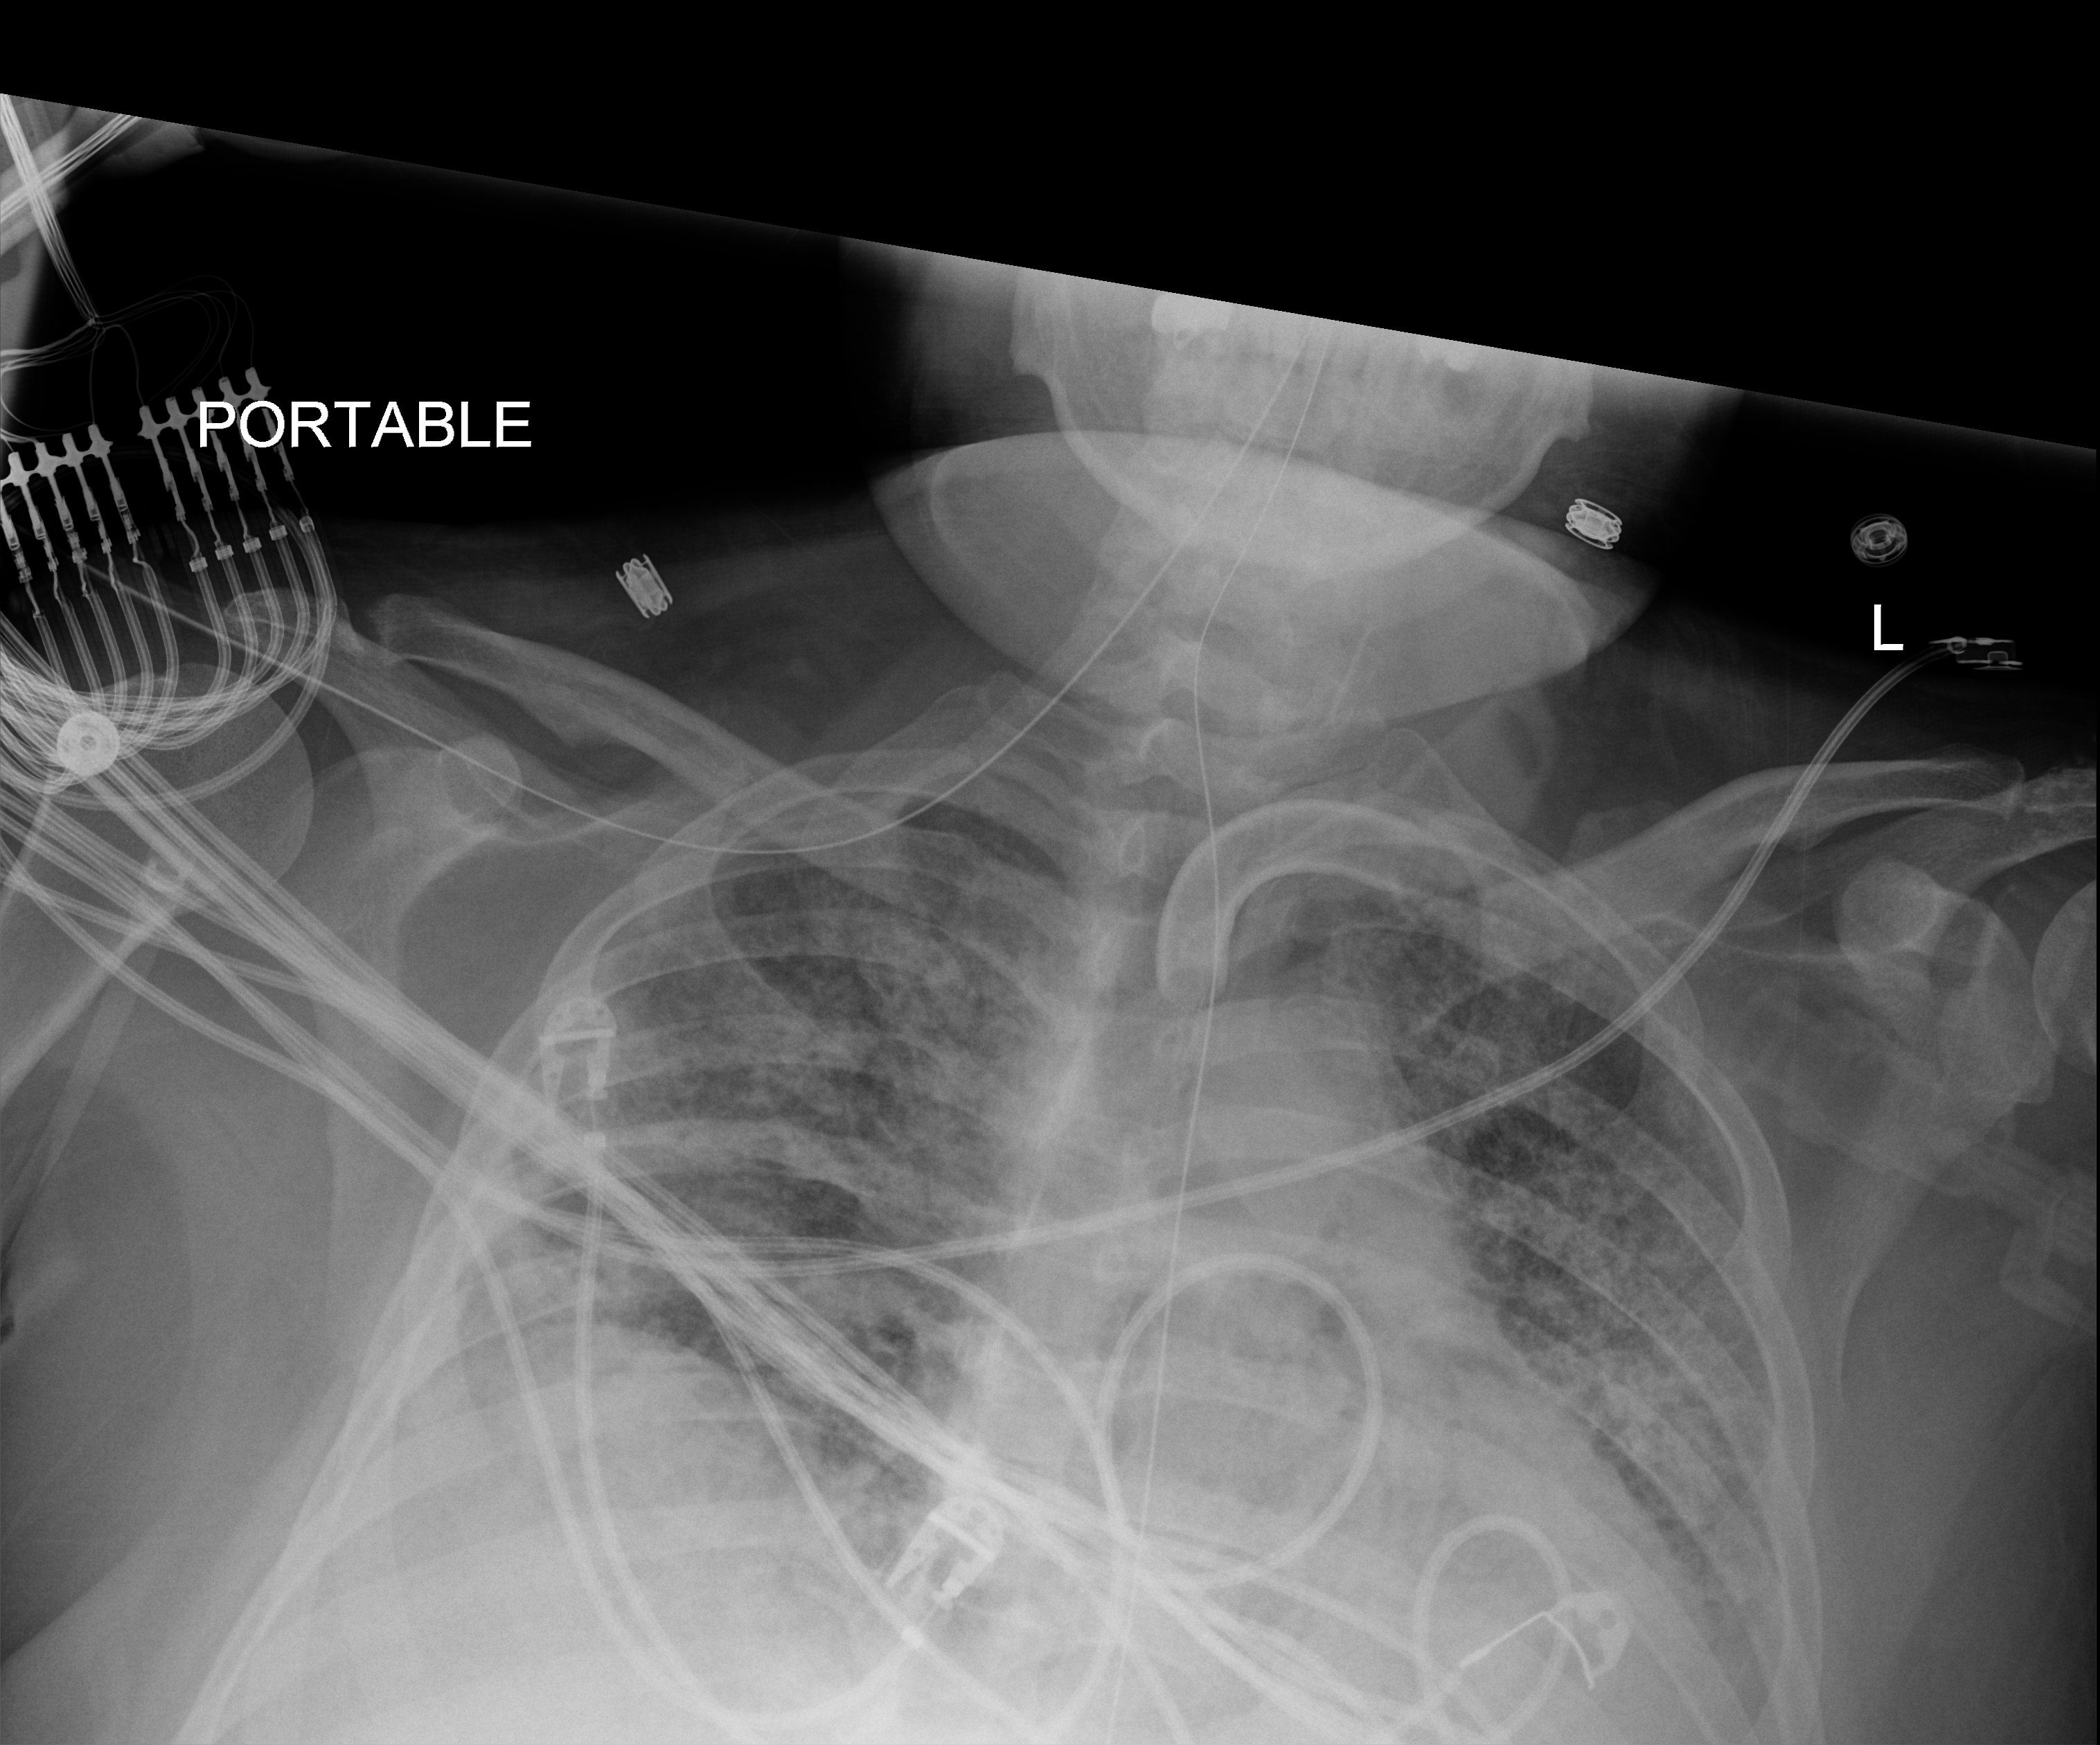
Chest X-ray (portable); anteroposterior (AP) projection. Patient hospitalised with COVID-19; male, aged 18–59 years.
Admission-level facts for this patient (not findings on this image; timing relative to this image not recorded): admitted to intensive care during this hospital stay: yes.